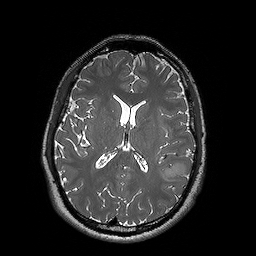
Brain MRI from a brain-tumour surgery series, one axial slice; position 78 of 192 along the scan axis; 1 mm slice thickness; 256 × 256 image matrix, field of view 250 × 250 mm. From the clinical record (not read from this slice): histopathology: Oligodendroglioma; WHO grade: 2; IDH mutation: yes; tumour location: Left Posterior Temporal.
Structures marked on this image (outlined manually by an expert reader):
- tumour: bounding box (x1, y1, x2, y2) in pixels: (159, 163, 193, 181)